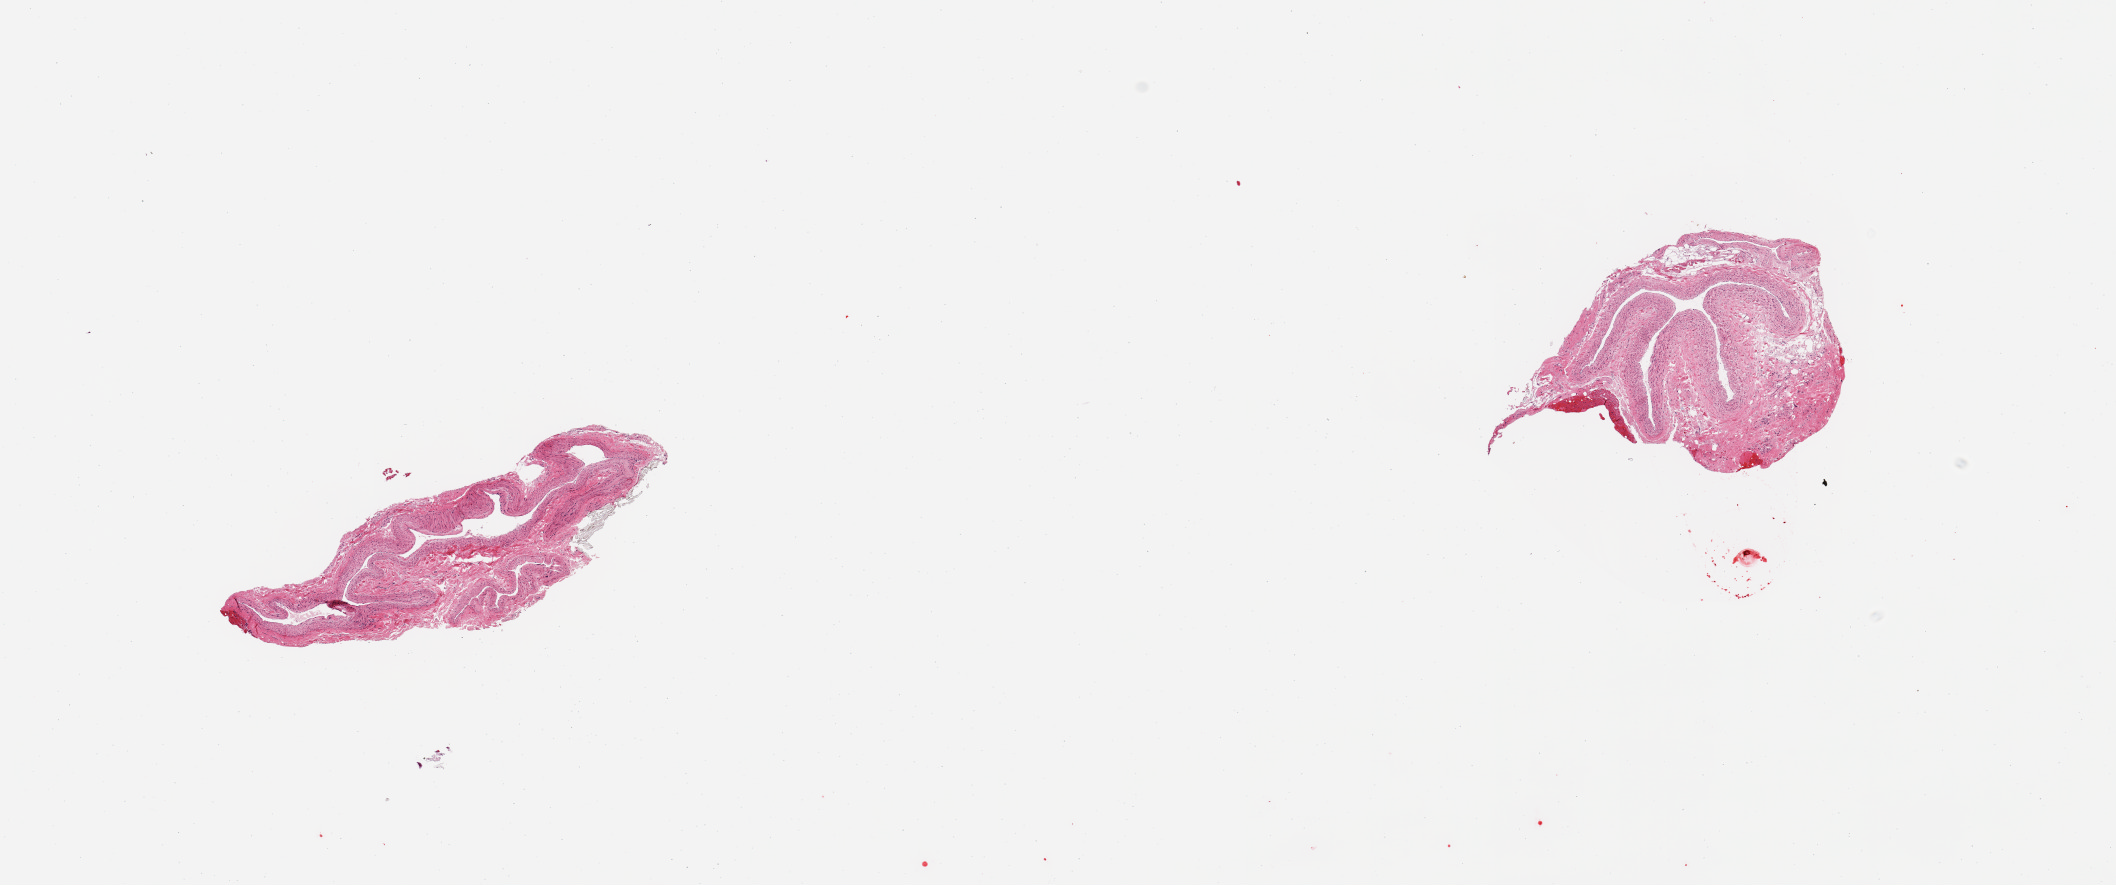
Whole-slide image, H&E stain — a low-resolution overview of the entire scanned area, about 16.7 x 7.0 mm, PAXgene-fixed, paraffin-embedded tissue, section of coronary artery (target tissue), tissue donor sample. Donor: male.
Reviewer comment on this tissue sample: 2 pieces, no significant atherosis.